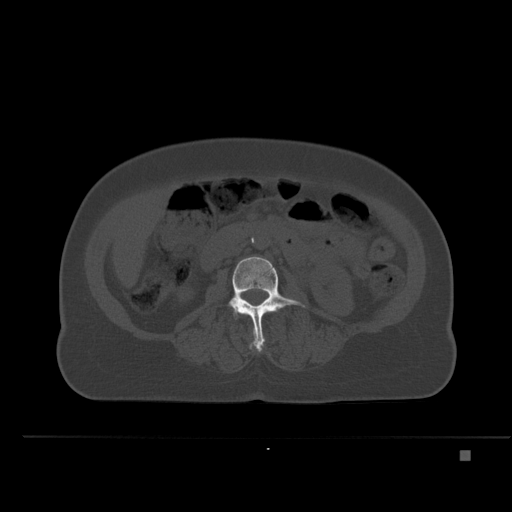
CT including the spine, one axial slice; bone window (W 1800 / L 400 HU); 1.5 mm slice thickness; 512 × 512 image matrix, field of view 422 × 422 mm. Patient: female, 74 years. Case-level facts recorded for this patient, not image findings: primary cancer: colon.
Annotated regions visible in this slice (semi-automatically segmented with operator editing):
- L3 vertebra: bounding box [x1, y1, x2, y2] px = [228, 257, 305, 351]